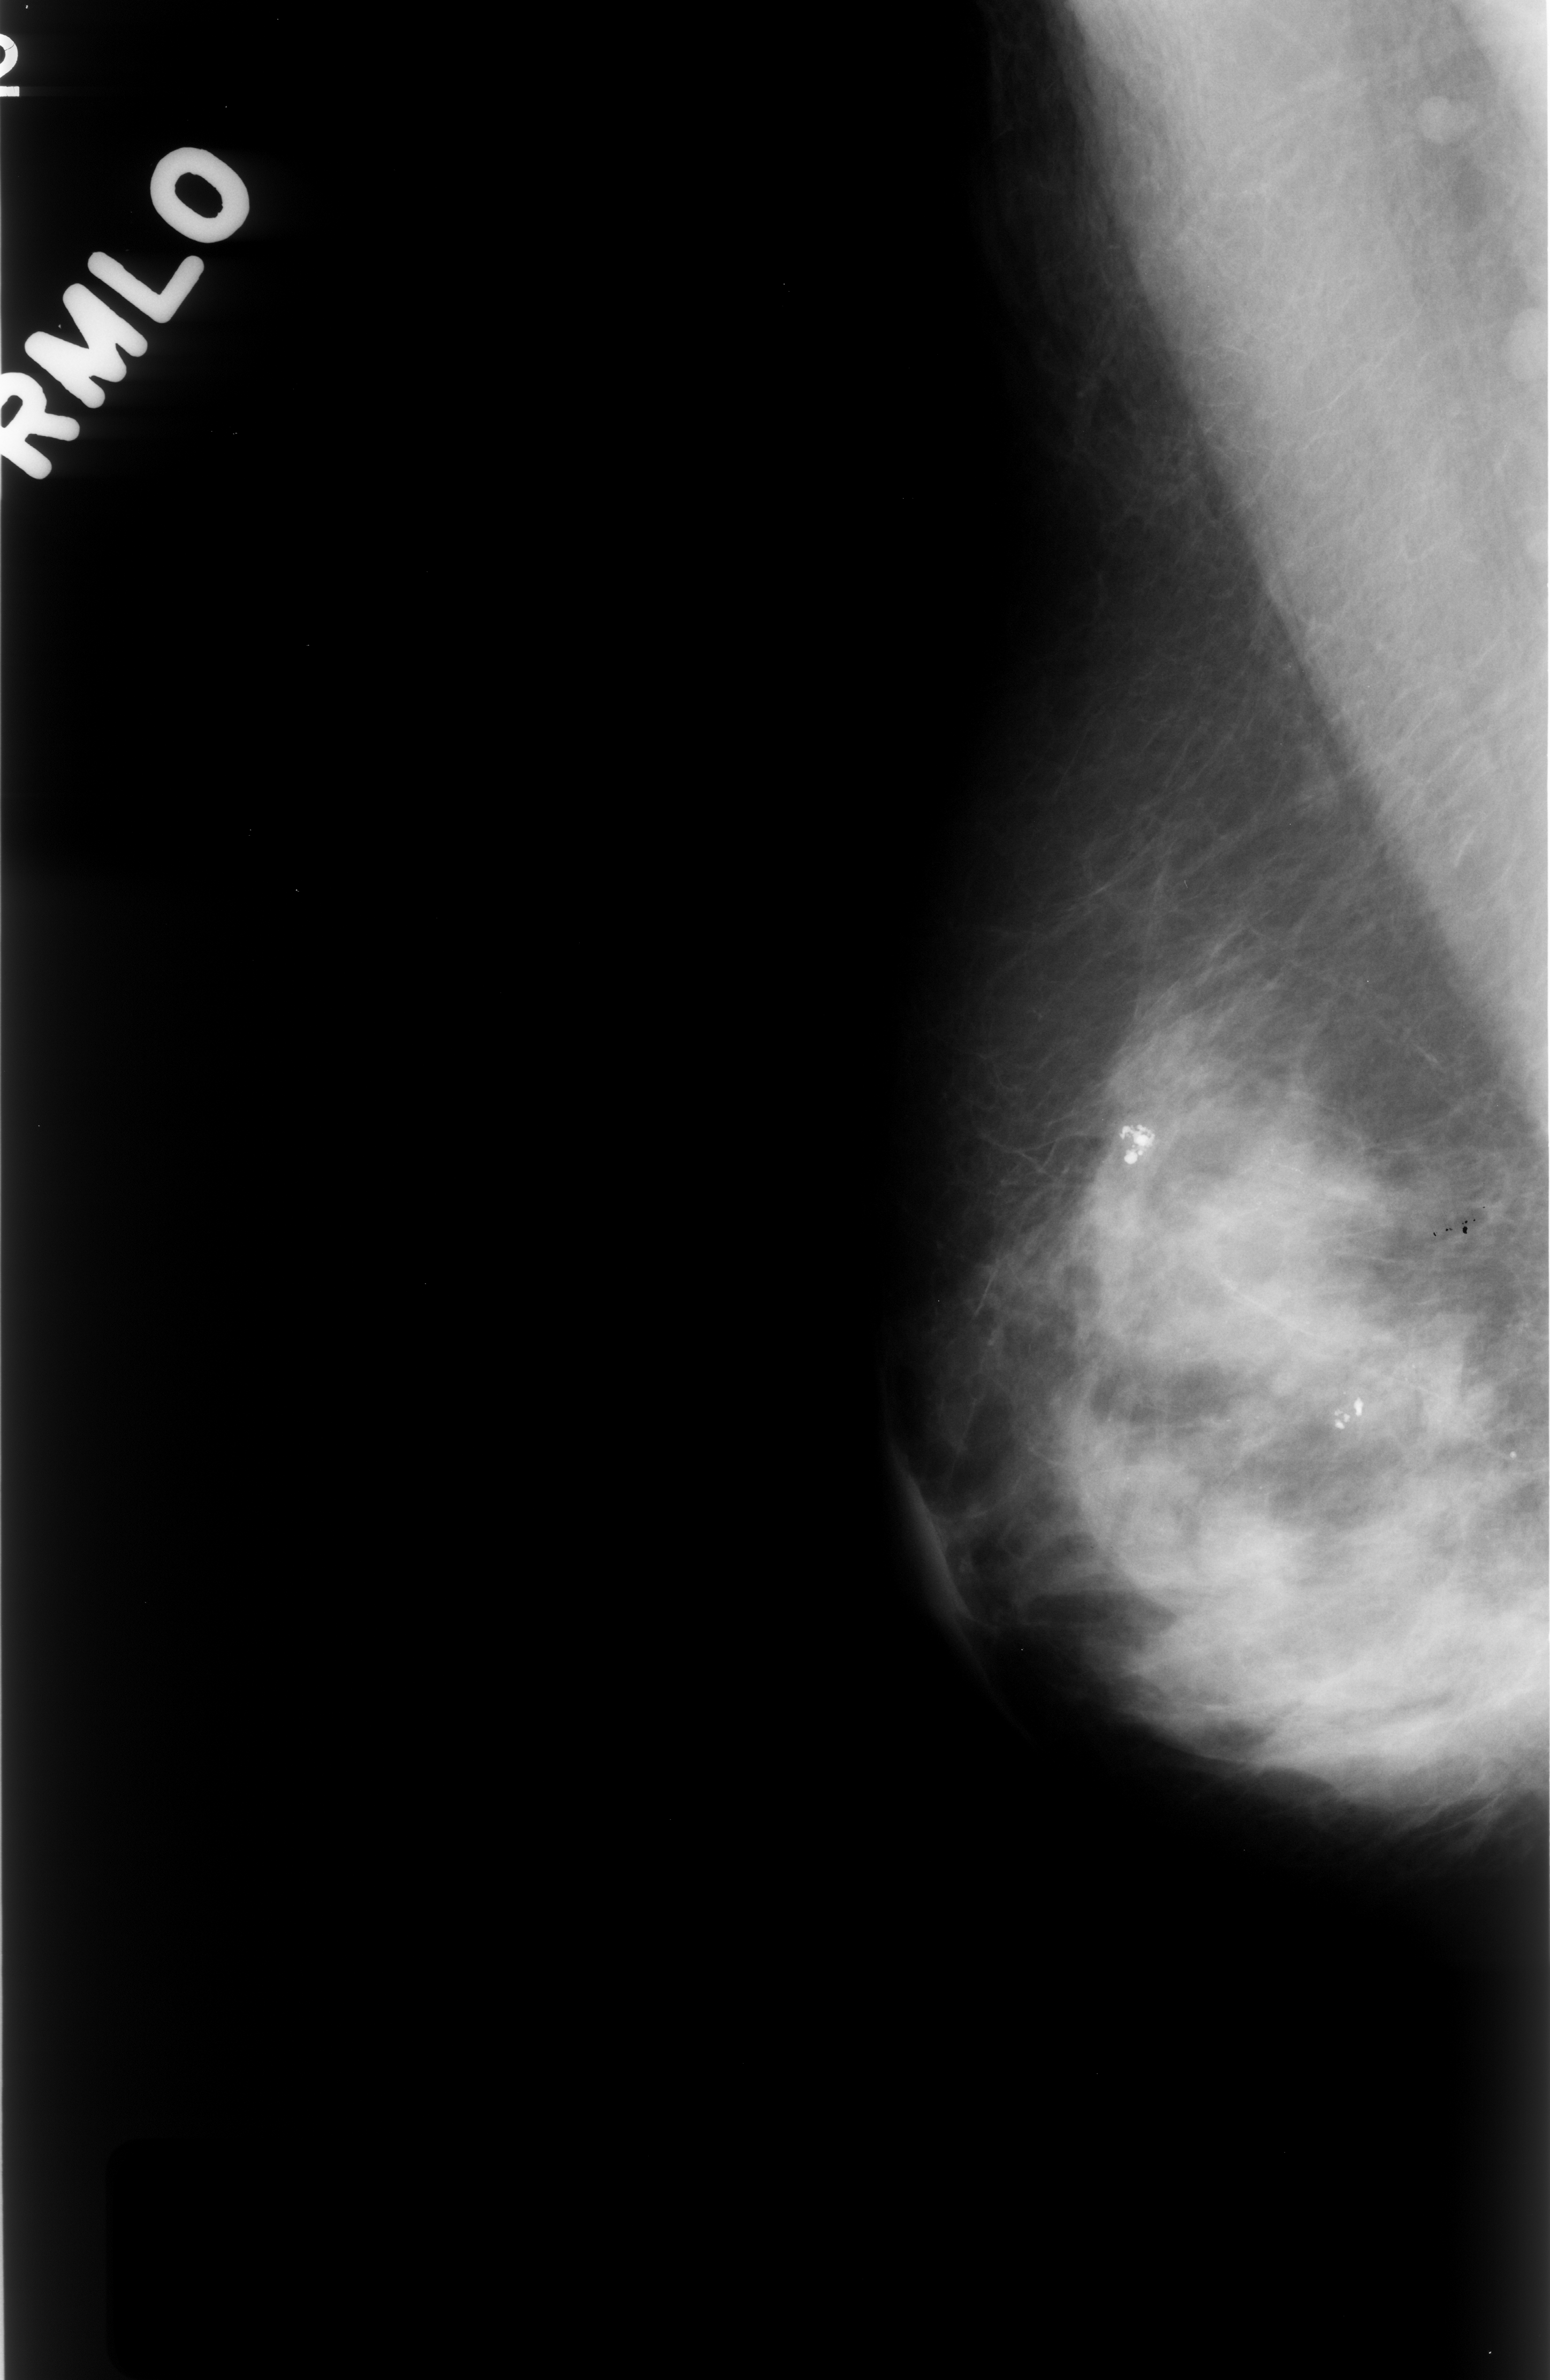
Mammogram (digitized film); right breast; MLO view; breast composition: heterogeneously dense (BI-RADS density category 3 of 4).
- Marked abnormality: calcifications, morphology amorphous, distribution clustered; BI-RADS assessment category 4; pathology (as recorded): benign.